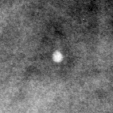
Crop from a digitized film mammogram around one marked abnormality; right breast; MLO view; BI-RADS breast density category 3 (scale 1–4).
Calcifications, morphology round and regular / lucent center; BI-RADS assessment category 2; benign; no additional work-up was recommended (benign without callback).